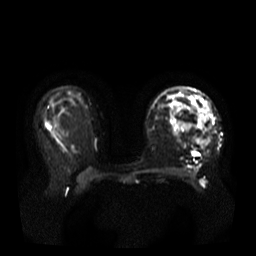
Breast MRI, one axial slice. Diffusion-weighted series; image 2 of 4 stored at this slice position (different b-values; order by instance number). 3 T. 5 mm slice thickness. 256 × 256 image matrix, field of view 380 × 380 mm. Female patient.
Outlined on this slice (manually delineated by an expert):
- tumour on diffusion-weighted imaging: bounding box (x1, y1, x2, y2) in pixels: (195, 104, 214, 149)